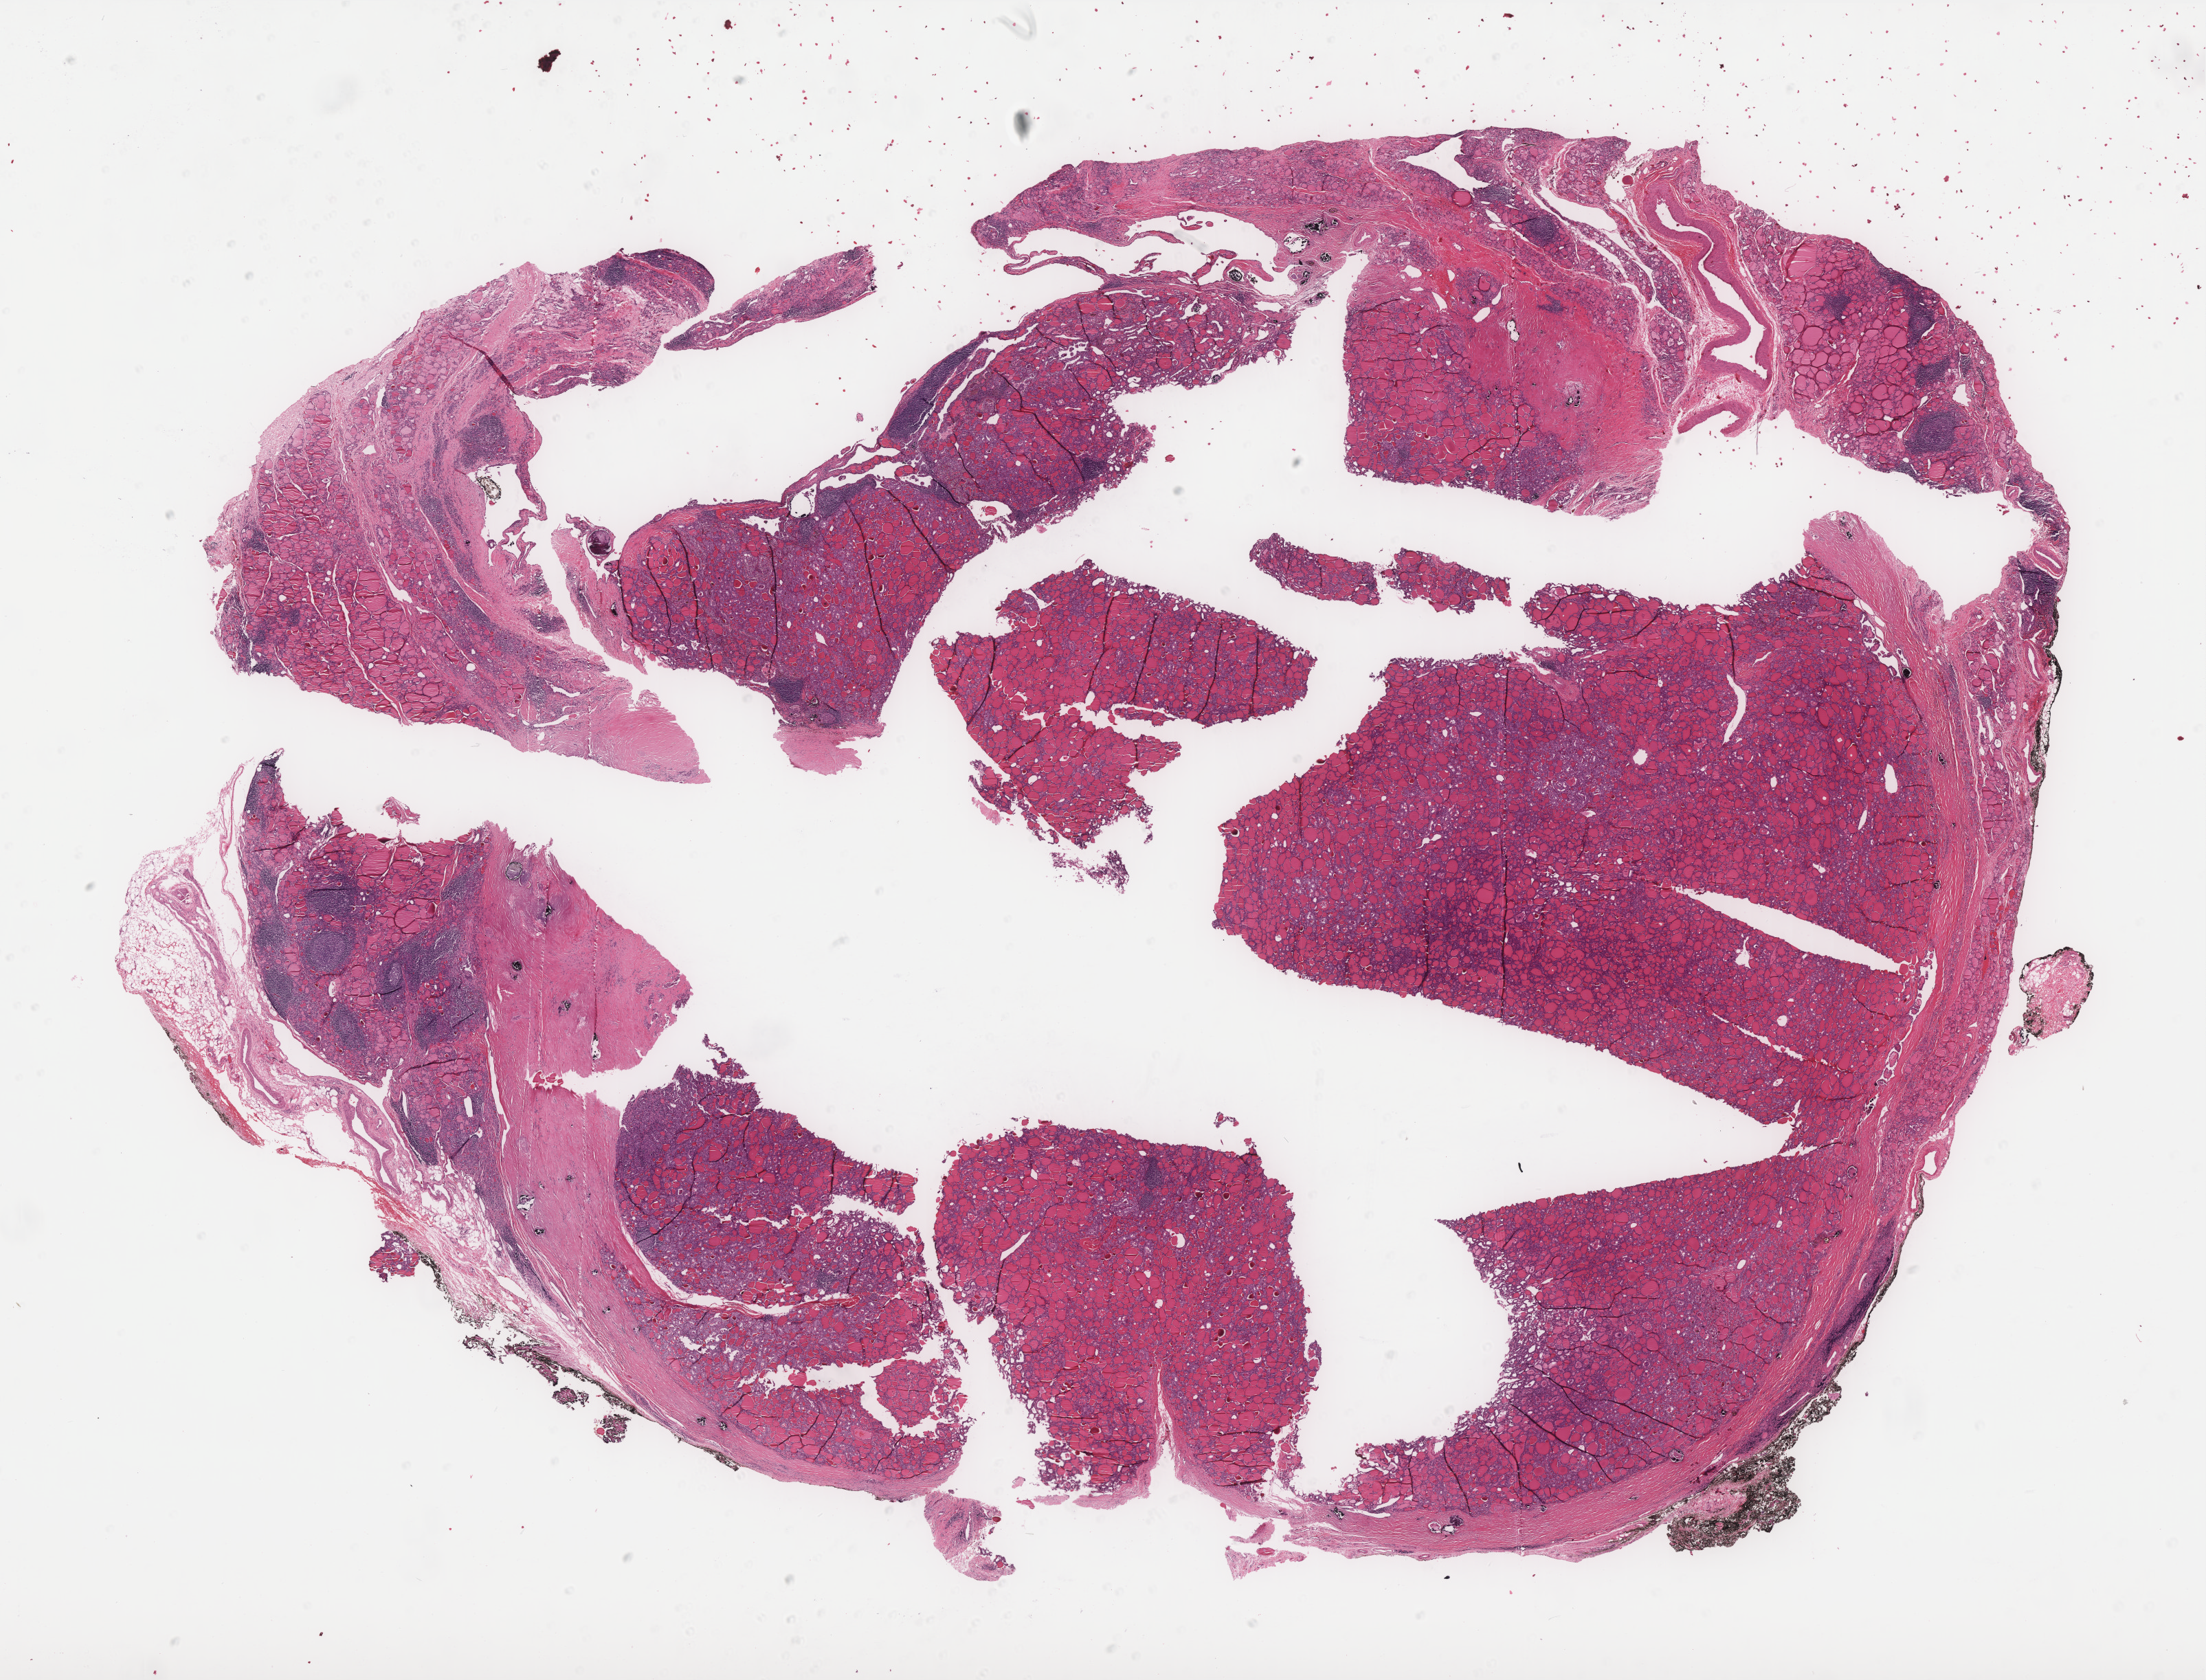
Digitized H&E tissue section (whole slide), low-resolution overview of the scanned area, about 25.7 x 19.6 mm (from a 40x scan), formalin-fixed paraffin-embedded (FFPE) diagnostic section, thyroid, primary tumour sample. Male patient; age at initial diagnosis 36 years.
- TNM: T2 N1a M0
- diagnosis: Papillary adenocarcinoma, NOS (thyroid gland)
- lymph nodes positive (case pathology): 1 of 8 examined
- AJCC pathologic stage: I (7th edition)